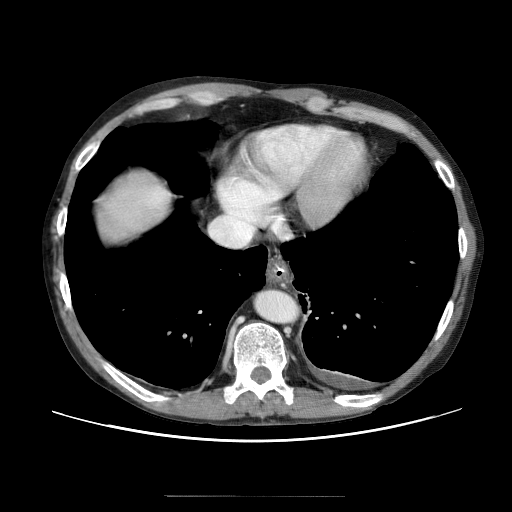
Contrast-enhanced abdominal CT (liver protocol), one axial slice; position 59 of 69 along the scan axis; 120 kVp; soft-tissue window (W 400 / L 40 HU); 2.5 mm slice thickness; 512 × 512 image matrix, field of view 380 × 380 mm. Case-level facts recorded for this patient, not image findings: diagnosis: hepatocellular carcinoma (patient treated with transarterial chemoembolisation; whether this scan precedes or follows treatment is not stated here); TNM stage (as recorded): Stage-IVB; Child-Pugh class: B; tumour differentiation: poorly differentiated; tumour nodularity: multinodular.
Structures marked on this image (semi-automatic segmentation, software-assisted and operator-edited):
- liver parenchyma outside the tumour (the mass and vessels are separate outlines, so this box may not span the whole liver): bounding box [x1, y1, x2, y2] px = [86, 168, 178, 258]